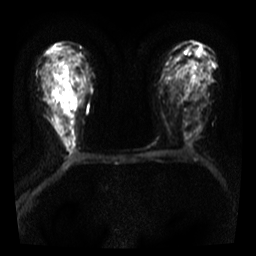
Breast MRI, one axial slice; position 21 of 36 along the scan axis; diffusion-weighted series; image 2 of 4 stored at this slice position (different b-values; order by instance number); 3 T; 5 mm slice thickness; 256 × 256 image matrix, field of view 300 × 300 mm. Female patient.
Structures marked on this image (expert manual segmentation):
- tumour on diffusion-weighted imaging: bounding box <56,65,71,94> (left, top, right, bottom; pixels)